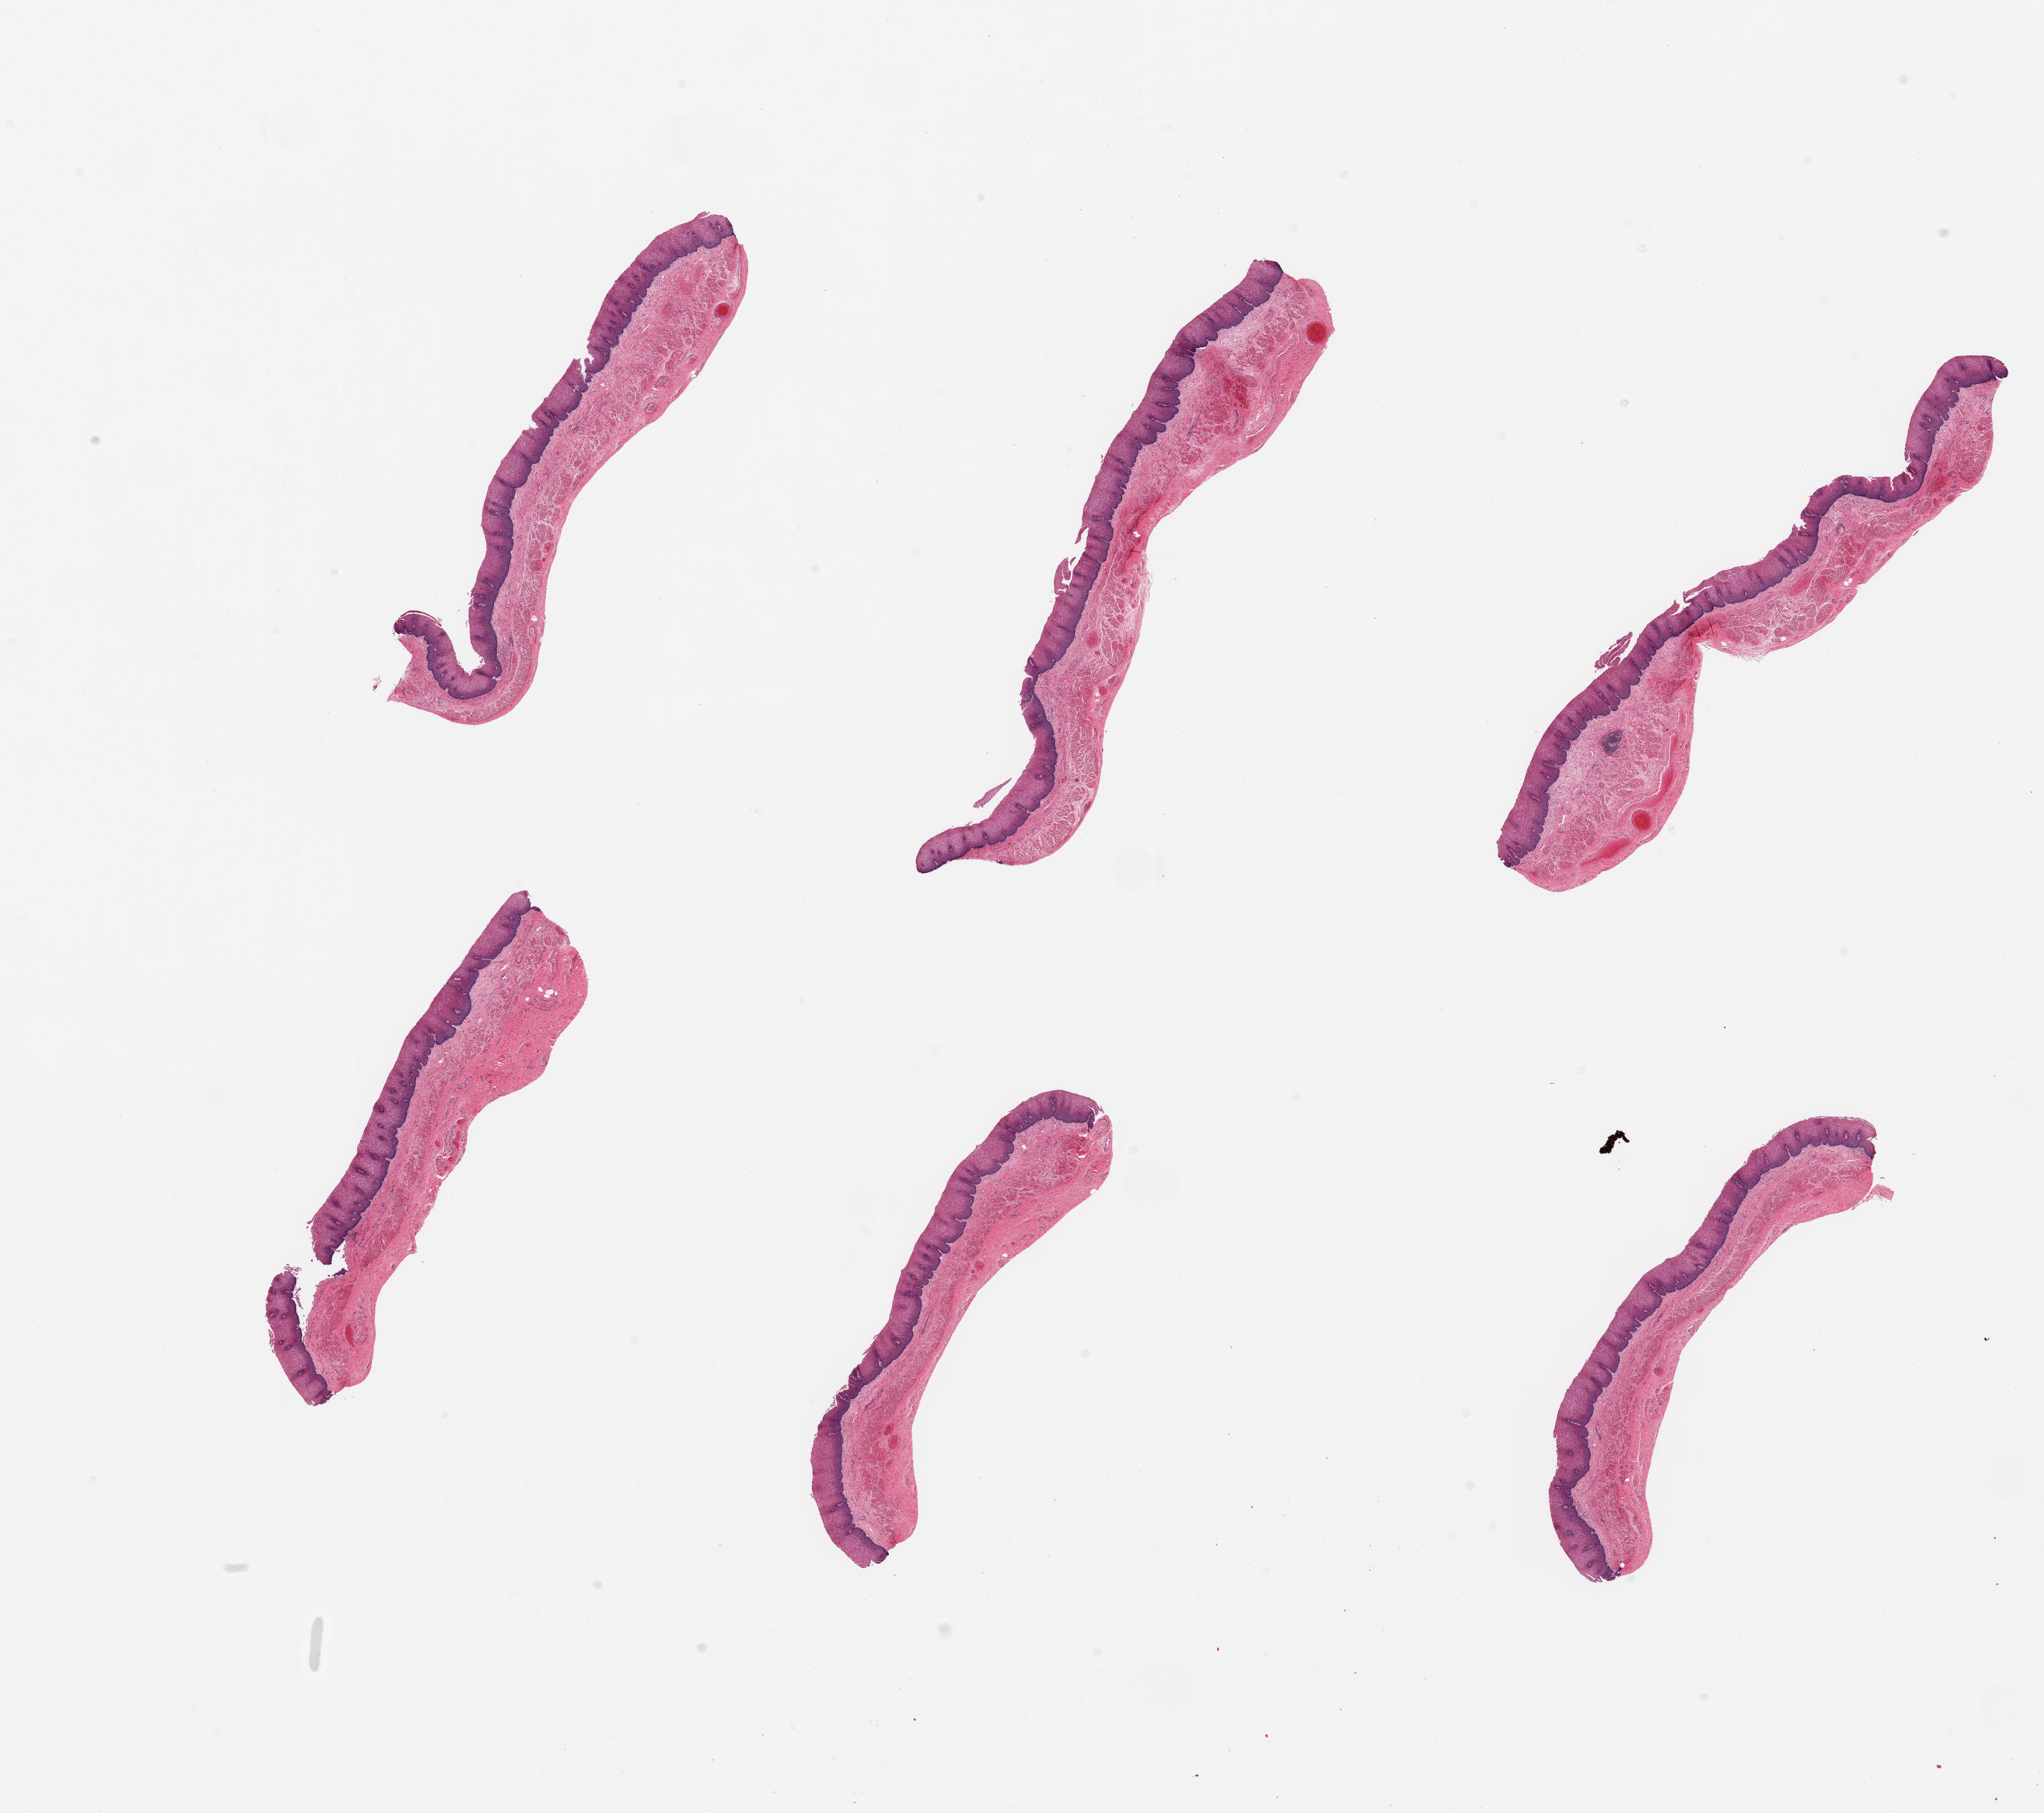
Digitized H&E-stained section — low-resolution overview of the scanned area, about 22.6 x 20.1 mm (slide scanned at 20x). PAXgene-fixed paraffin-embedded (PFPE) section. Sampled site (target tissue): esophageal mucous membrane. Tissue donor sample.
Review note (as recorded): 6 pieces; well dissected.